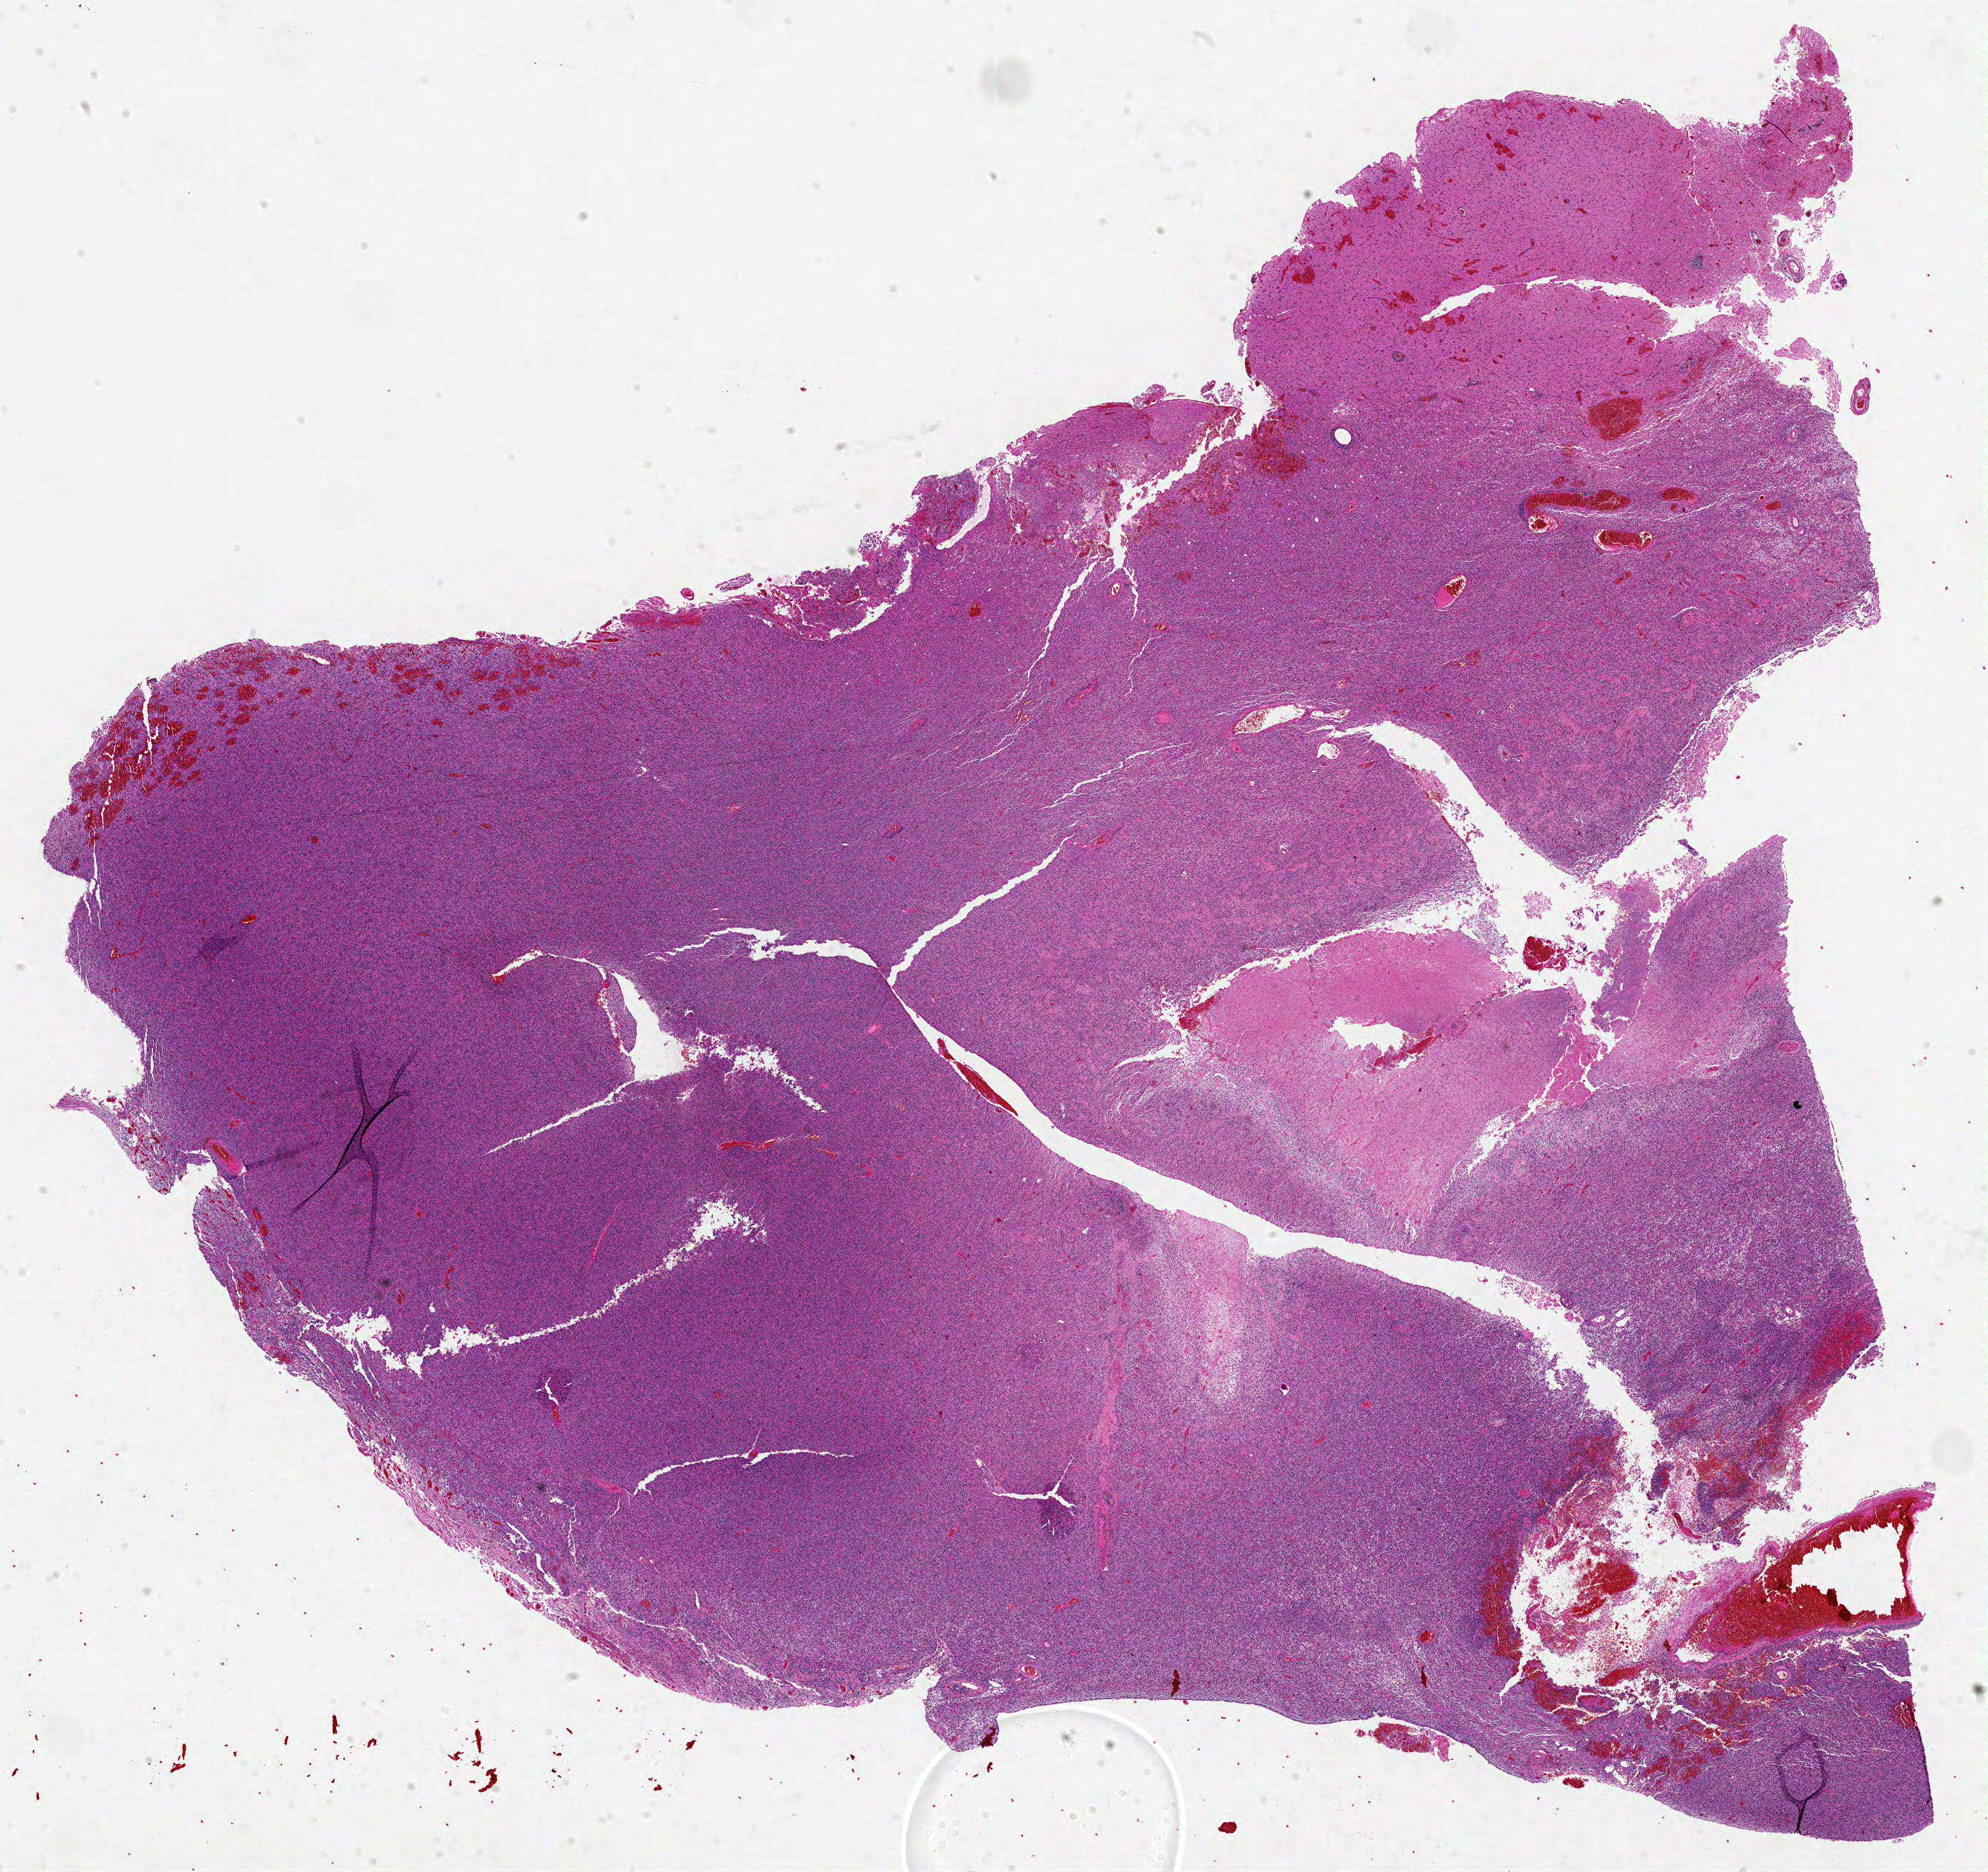
Digitized Hematoxylin and eosin (H&E) stained tissue section (whole slide) — shown as a low-resolution overview of the whole scanned area (about 22.0 x 20.7 mm). Formalin-fixed paraffin-embedded (FFPE) diagnostic section. Sample: primary tumour, brain. Male, age 60 years at initial diagnosis.
• diagnosis: Glioblastoma